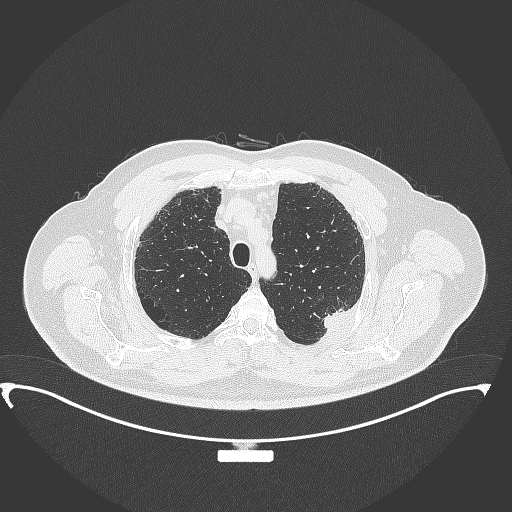
Chest CT, one axial slice; position 290 of 350 along the scan axis; reconstruction kernel B70f; 120 kVp; lung window (W 1500 / L -600 HU); 1 mm slice thickness; 512 × 512 image matrix. Patient: male, 64 years. Case-level facts recorded for this patient, not image findings: clinical TNM (as recorded): T1c N1 M1.
Outlined on this slice (rectangle marked by the reading radiologist):
- lung tumour (recorded histology: adenocarcinoma): bounding box <314,301,359,342> (left, top, right, bottom; pixels)